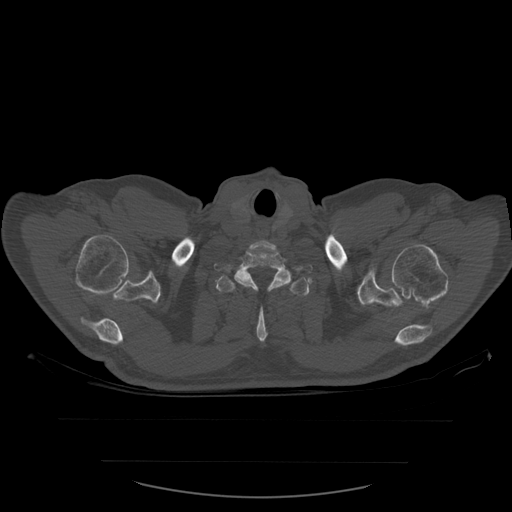
CT including the spine, one axial slice; bone window (W 1800 / L 400 HU); 512 × 512 image matrix. Patient age 71 years. Case-level facts recorded for this patient, not image findings: primary cancer: lung; vertebrae with lytic lesions (as recorded): T1, T2, L5, S1.
Annotated regions visible in this slice (semi-automatic segmentation, software-assisted and operator-edited):
- T1 vertebra: bounding box <214,246,313,291> (left, top, right, bottom; pixels)
- T2 vertebra: <216,265,312,343>